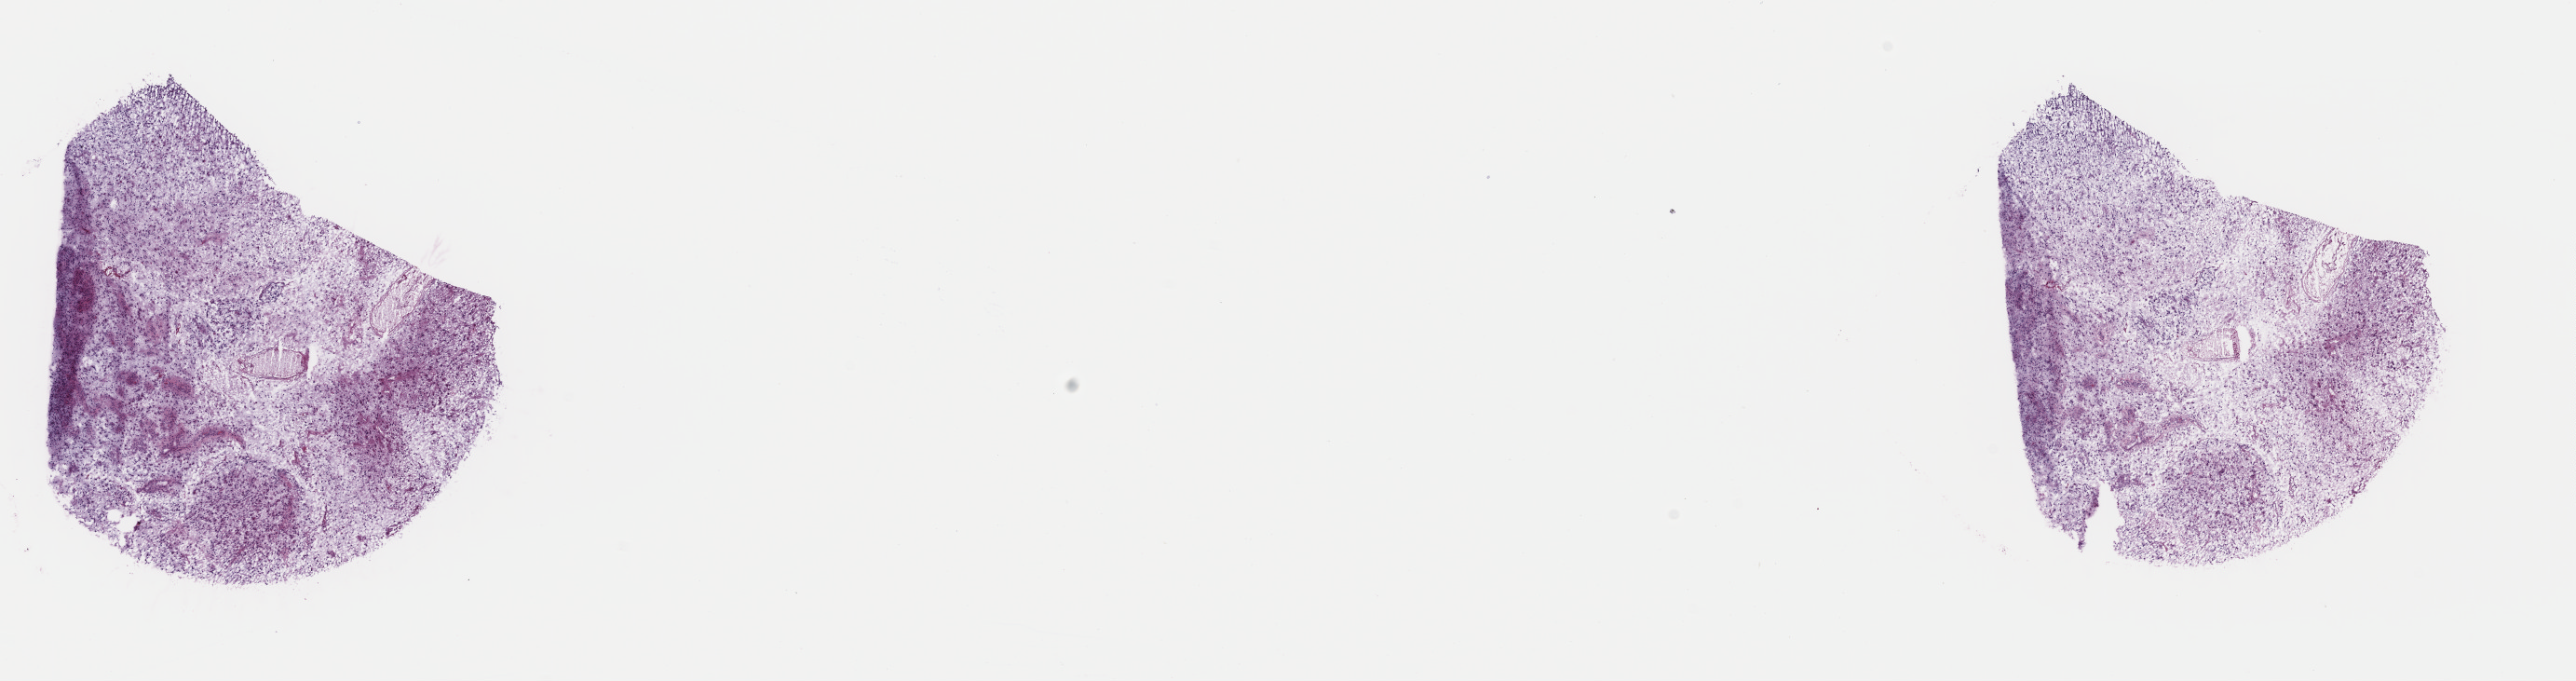
H&E whole-slide image — shown as a low-resolution overview of the whole scanned area (about 21.8 x 5.8 mm, from a 40x scan); frozen section from the top of the tissue portion; sample: primary tumour, brain. Male patient; age at initial diagnosis 79 years. Composition of this section per pathologist review: tumour cells 30%, tumour nuclei 80%, normal cells 10%, stromal cells 60%, necrosis 0%. Inflammatory infiltration, as recorded: lymphocyte infiltration 0%, monocyte infiltration 0%, neutrophil infiltration 0%.
Pathologic diagnosis: Glioblastoma.